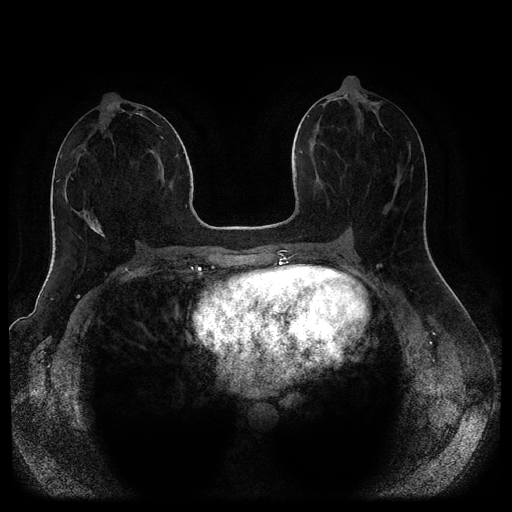
Breast MRI (dynamic contrast-enhanced, multi-phase), one axial slice; dynamic contrast-enhanced series, time point 2 of 5 at this slice position (early post-contrast); 1.5 T; TE 2.6 ms, TR 5.3 ms; 2 mm slice thickness; 512 × 512 image matrix, field of view 370 × 370 mm. Patient: female, 44 years.
Outlined on this slice (semi-automatically segmented with operator editing):
- breast lesion (labelled benign in the annotation): box from (x=88, y=219) to (x=105, y=237) px